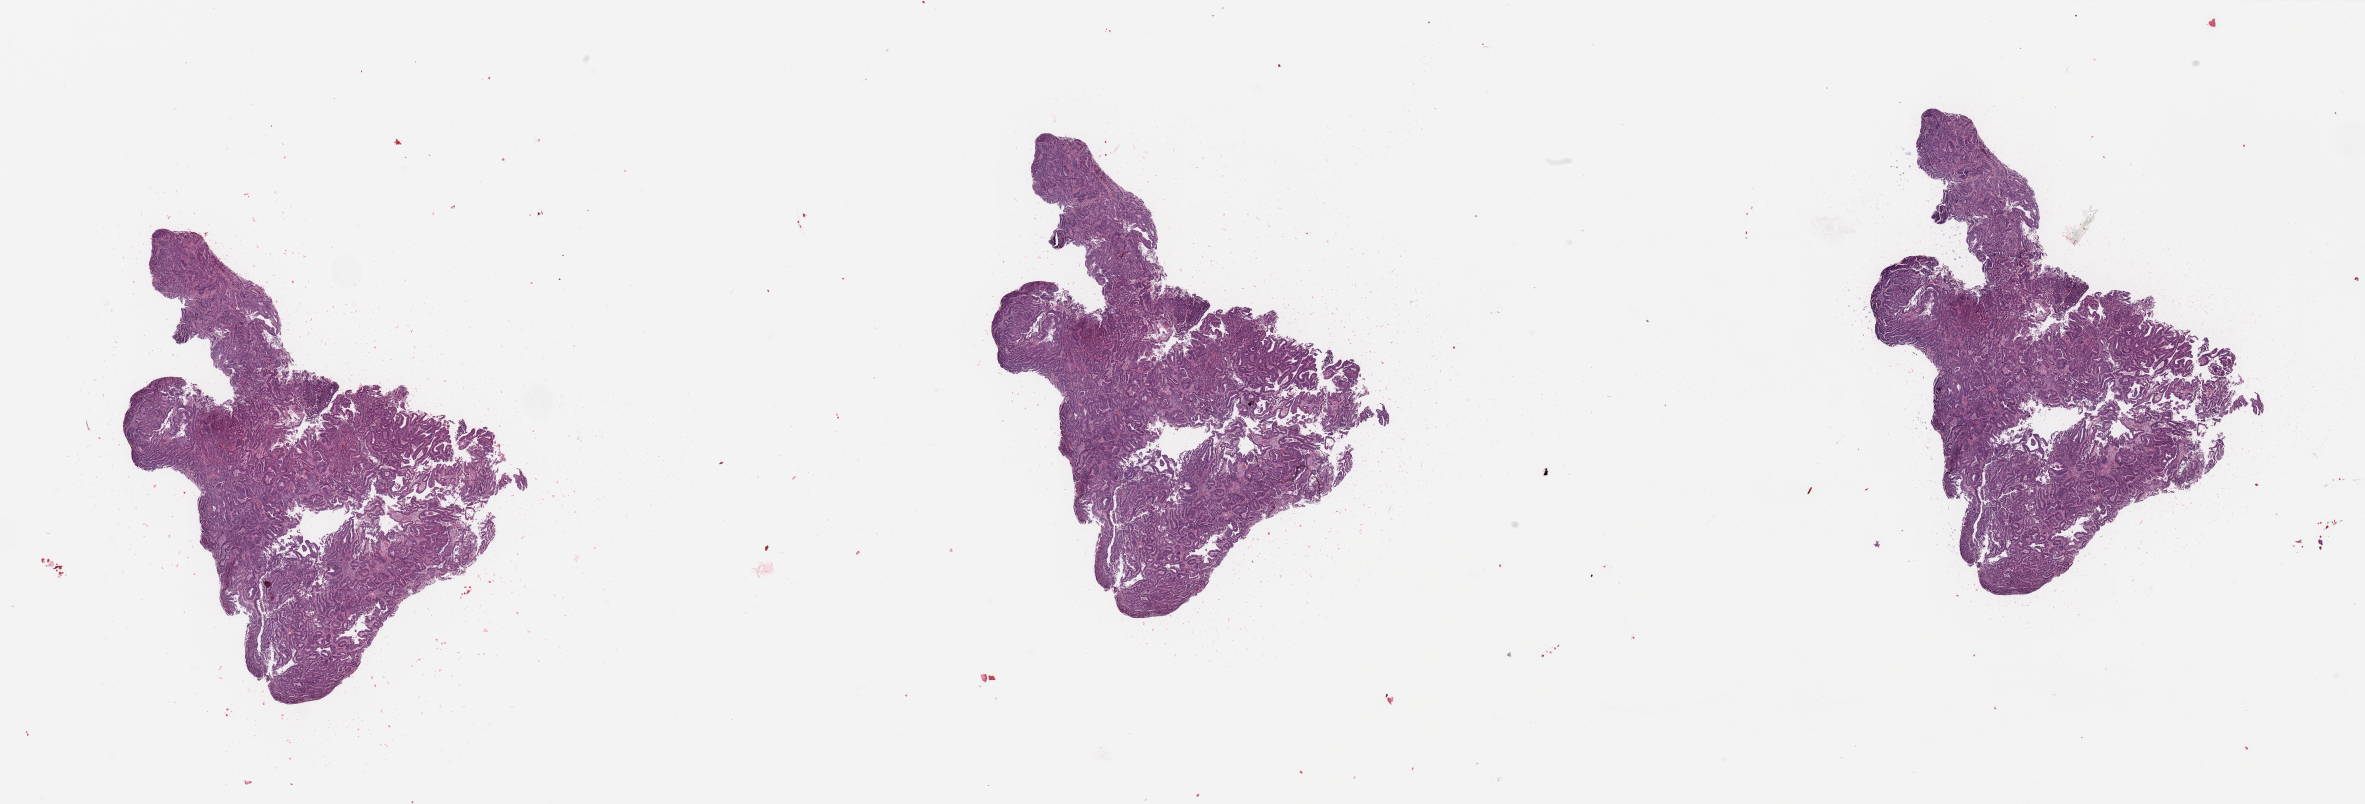
H&E-stained whole-slide image, a low-resolution overview of the entire scanned area, about 37.4 x 12.7 mm (from a 20x scan). Tumour tissue sample, sampled site: uterus. Patient: female, age 53 years. Composition of this section per pathologist review: tumour nuclei 90%, necrosis 0%.
Histologic diagnosis: Endometrioid adenocarcinoma, NOS.